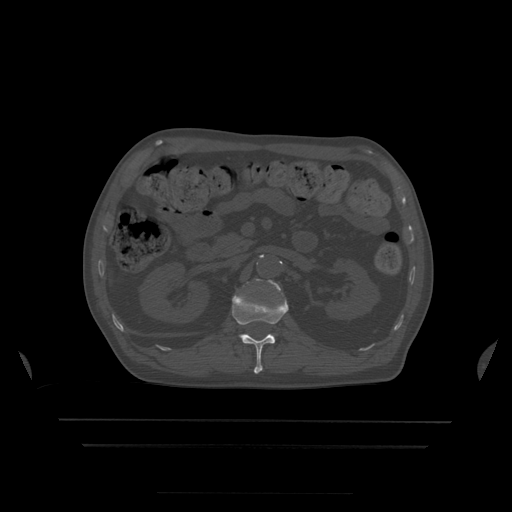
CT including the spine, one axial slice. Position 166 of 522 along the scan axis. Bone window (W 1800 / L 400 HU). 1.25 mm slice thickness. 512 × 512 image matrix, field of view 436 × 436 mm. Patient age 68 years. From the clinical record (not read from this slice): primary cancer: urothelial.
Structures marked on this image (semi-automatic segmentation, software-assisted and operator-edited):
- L1 vertebra: bounding box (x1, y1, x2, y2) in pixels: (232, 286, 289, 374)
- L2 vertebra: (258, 280, 280, 289)